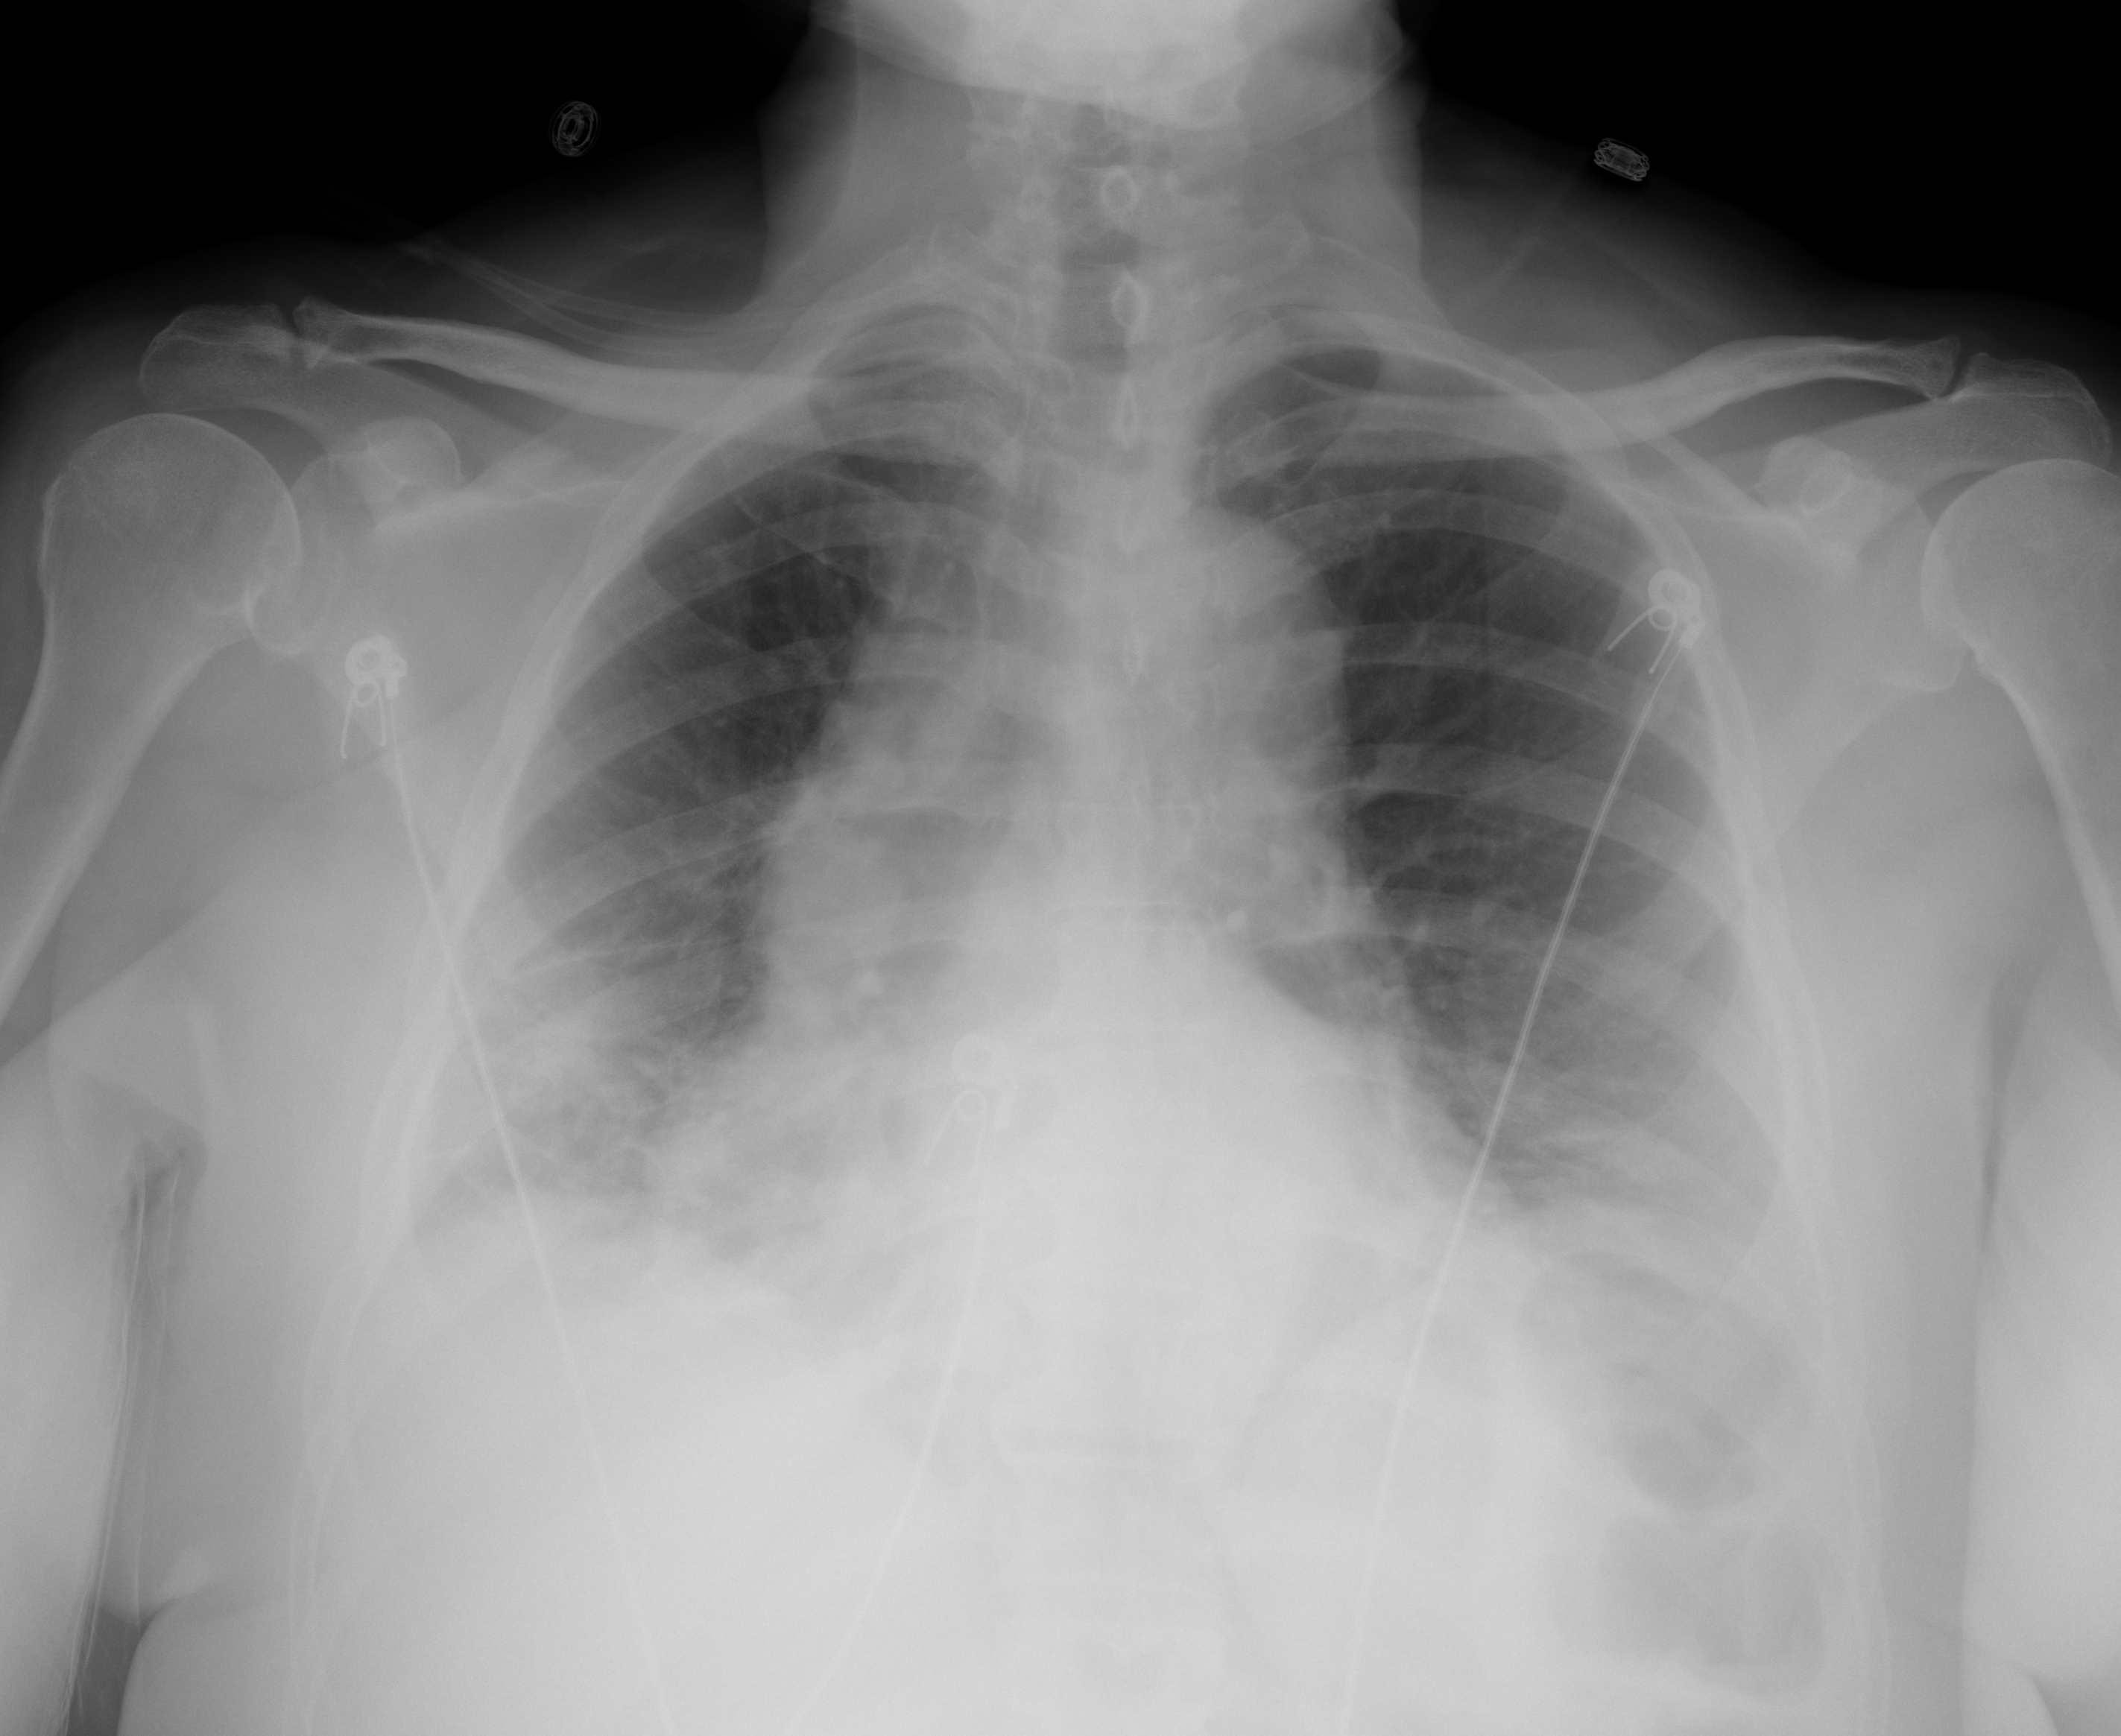
Portable chest radiograph, AP projection. Female patient, age 60 years; imaged 1 day after the COVID-19 diagnosis.
Key findings recorded by the radiologist: patchy airspace opacities in the bilateral lung bases, right greater than left.